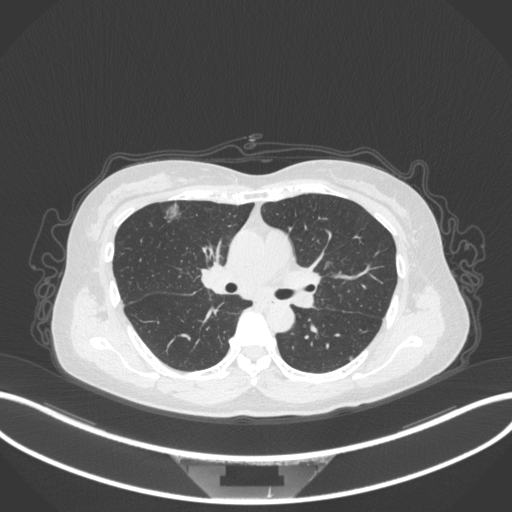
Chest CT, one axial slice; reconstruction kernel B31f; 120 kVp; lung window (W 1500 / L -600 HU); 1 mm slice thickness; 512 × 512 image matrix, field of view 400 × 400 mm. Patient: female, 61 years. Case-level facts recorded for this patient, not image findings: clinical TNM (as recorded): T1b N0 M0; histopathological grade: G1.
Structures marked on this image (bounding box drawn by a radiologist):
- lung tumour (recorded histology: adenocarcinoma): bounding box <161,200,179,225> (left, top, right, bottom; pixels)